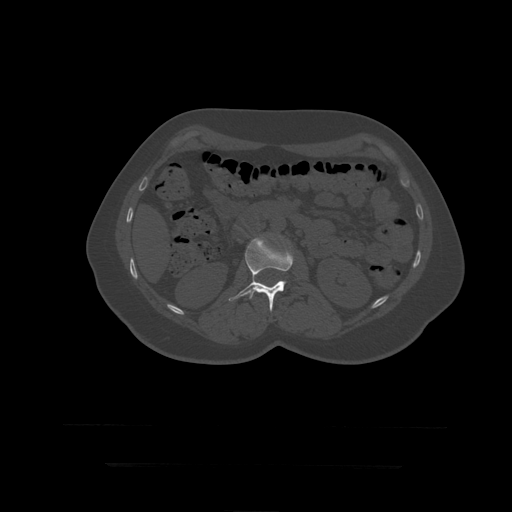
CT including the spine, one axial slice; position 146 of 399 along the scan axis; reconstruction kernel STANDARD; bone window (W 1800 / L 400 HU); 512 × 512 image matrix, field of view 450 × 450 mm. Patient age 41 years. From the clinical record (not read from this slice): primary cancer: breast.
Structures marked on this image (semi-automatically segmented with operator editing):
- L2 vertebra: bounding box [x1, y1, x2, y2] px = [229, 237, 294, 312]